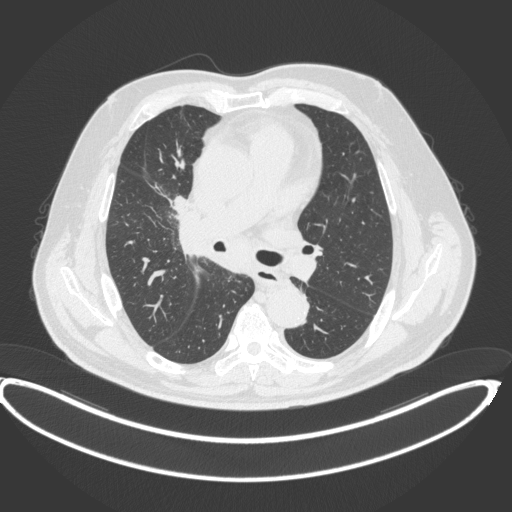
Chest CT, one axial slice. Slice 242 of 395 in the series (ordered by position). Reconstruction kernel B31f. 120 kVp. Lung window (W 1500 / L -600 HU). 512 × 512 image matrix, field of view 448 × 448 mm. Patient: male, 62 years. From the clinical record (not read from this slice): clinical TNM (as recorded): T1c N3 M1c.
Annotated regions visible in this slice (rectangle marked by the reading radiologist):
- lung tumour (recorded histology: adenocarcinoma): bounding box <168,195,189,216> (left, top, right, bottom; pixels)